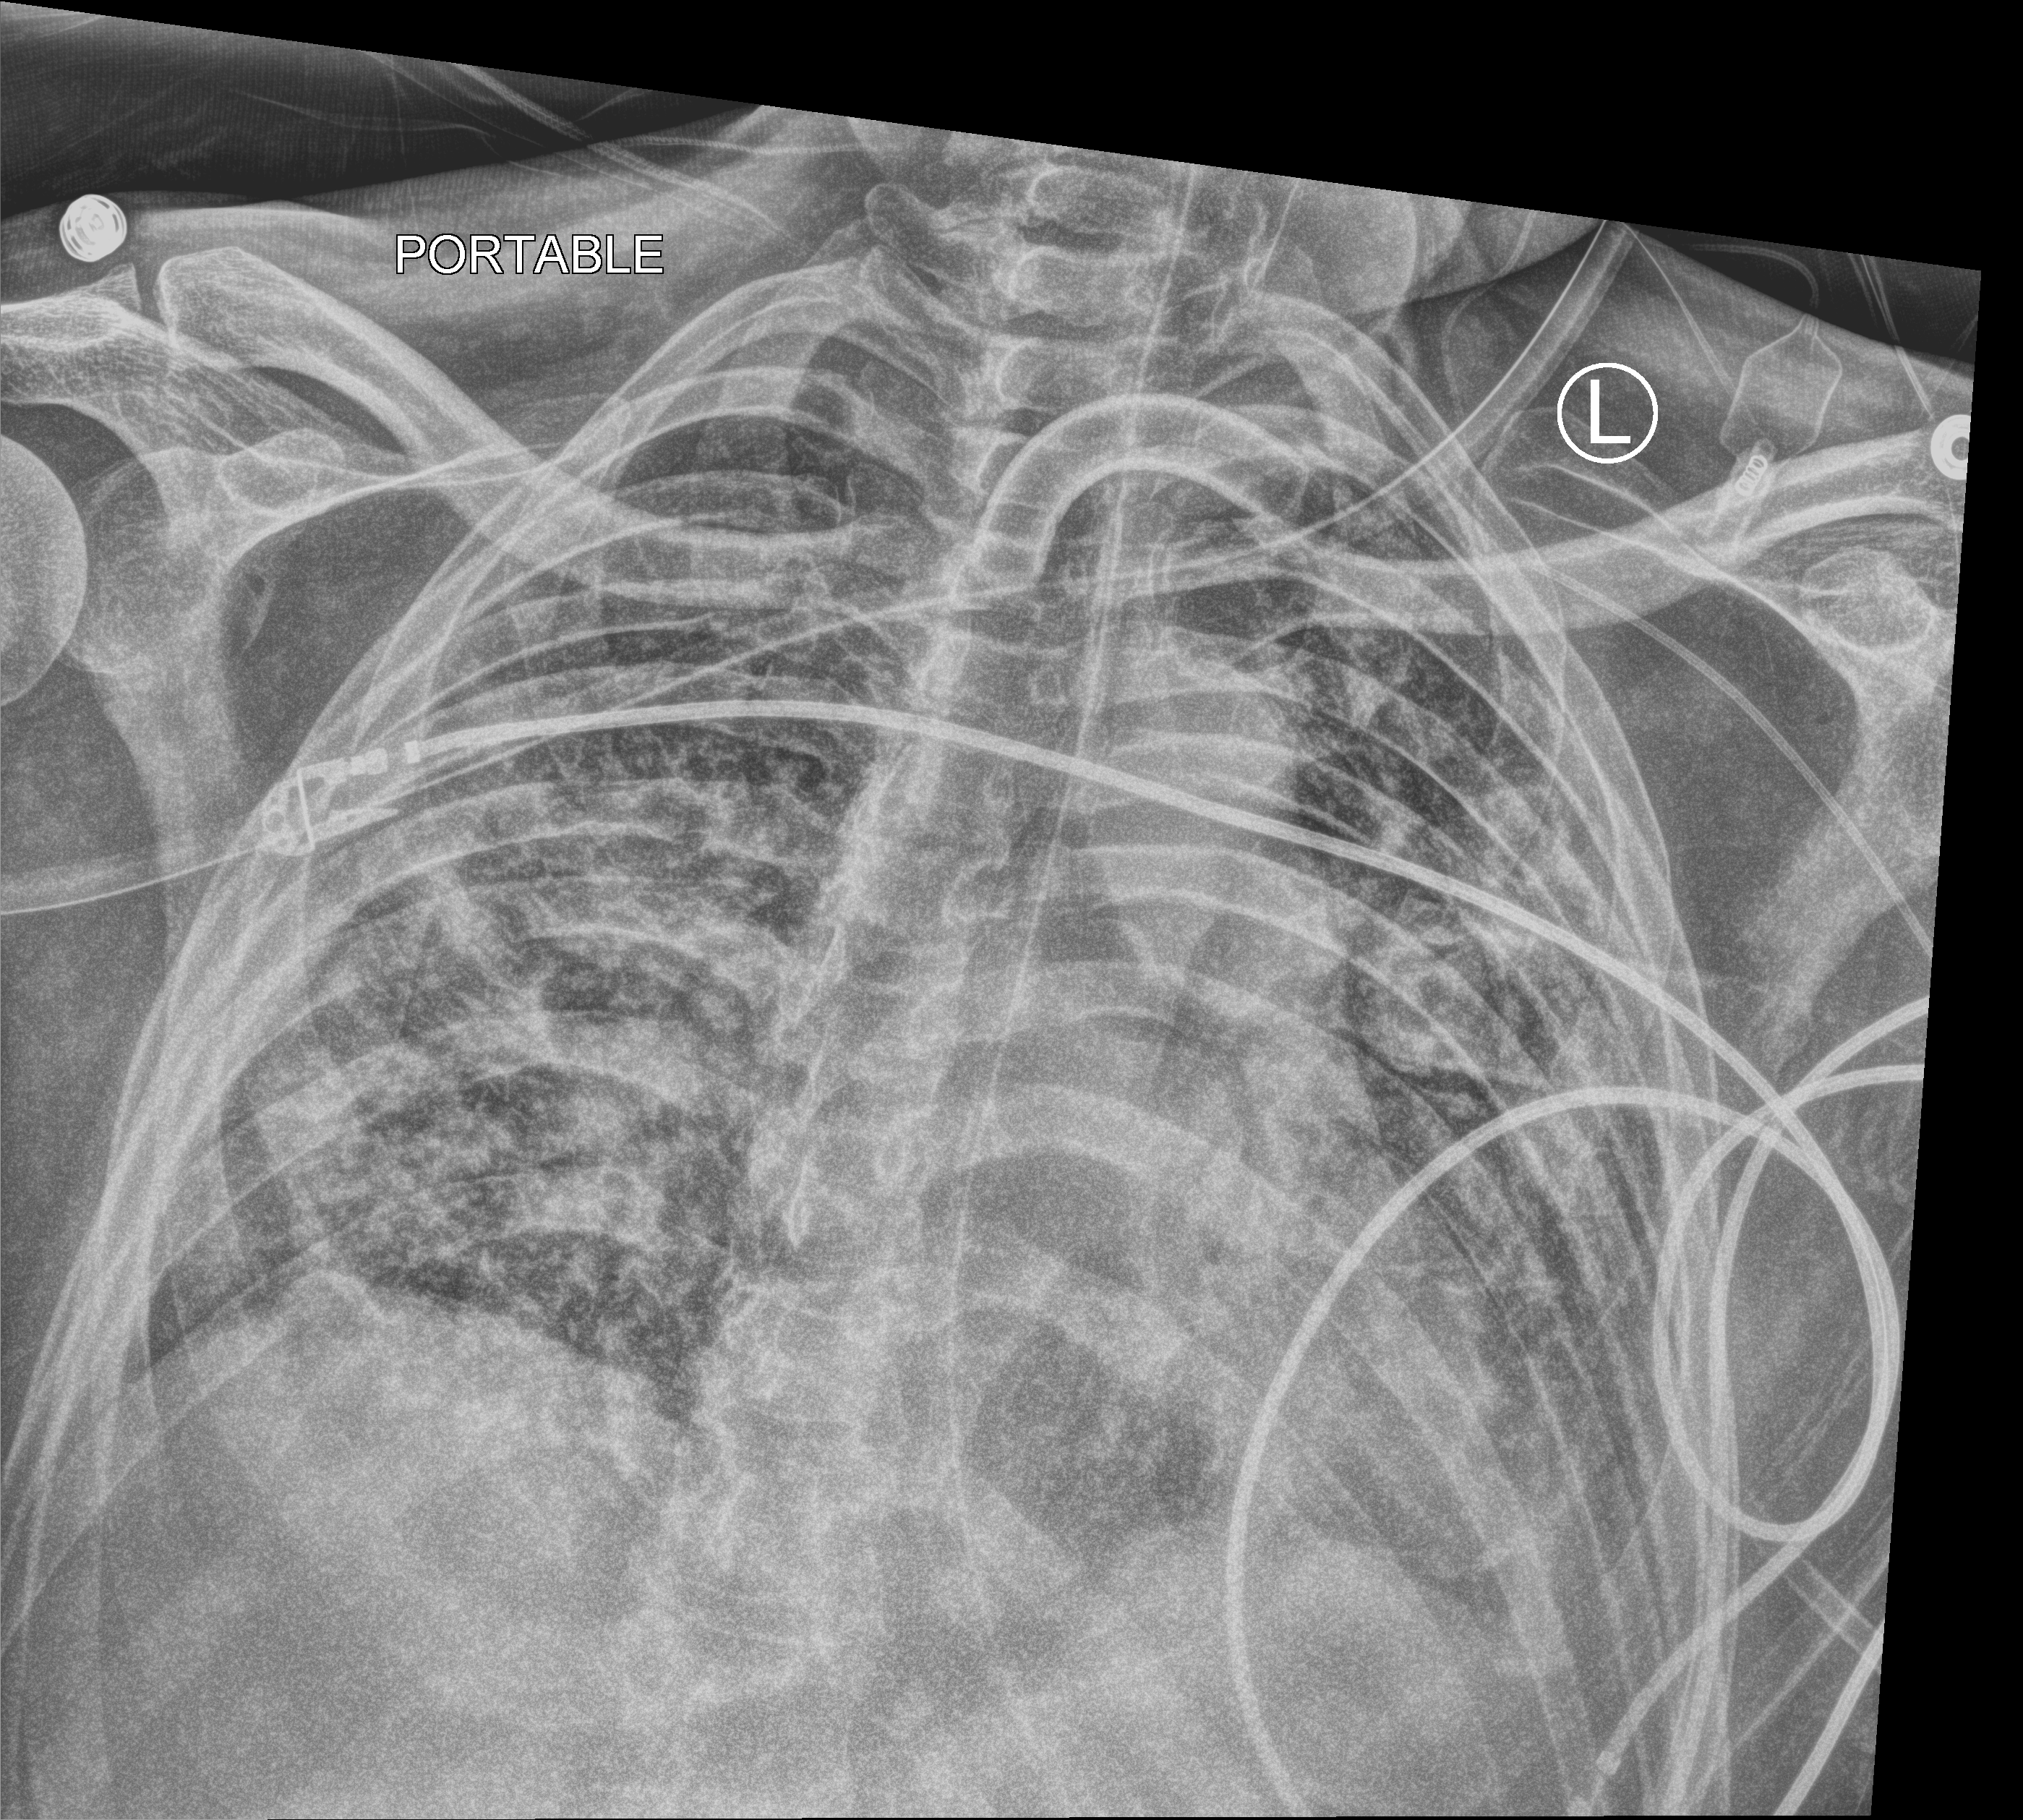
Chest X-ray (portable). Male patient hospitalised with COVID-19, age 18–59 years.
Admission-level facts for this patient (not findings on this image; timing relative to this image not recorded): mechanically ventilated during this hospital stay: yes; length of hospital stay: 75 days.